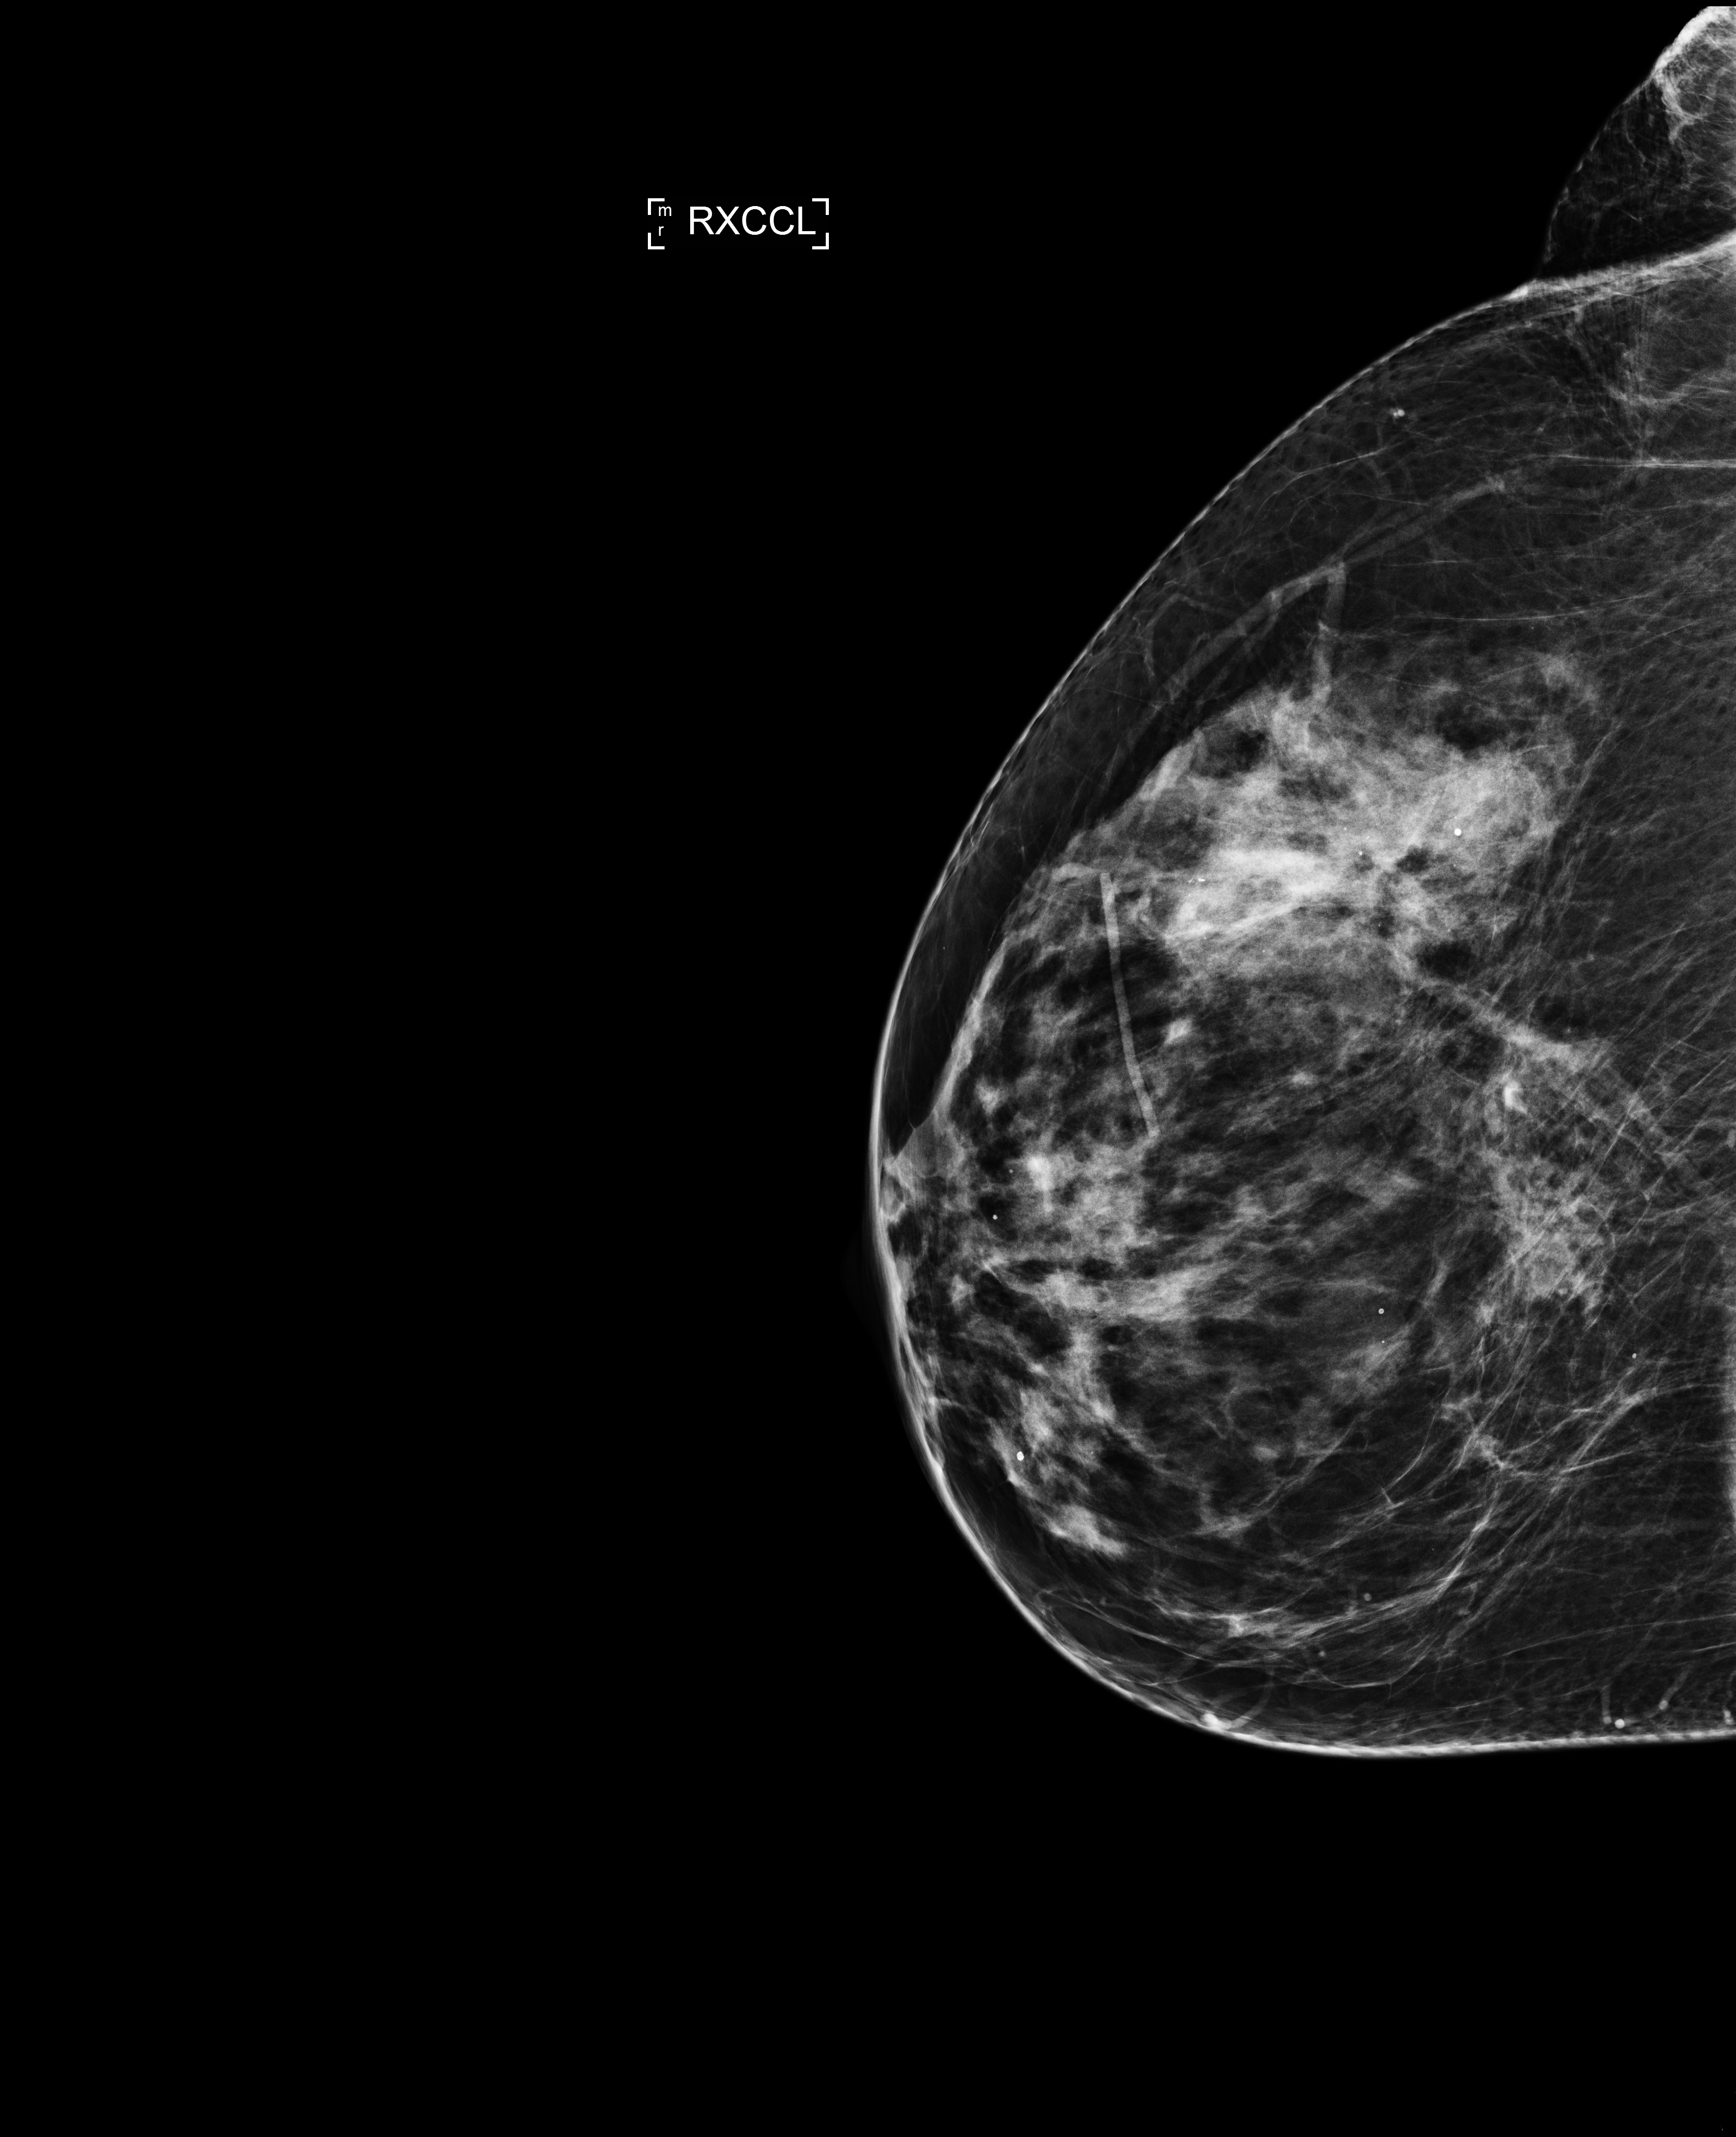
Screening examination, compressed breast thickness 68 mm. Patient: female, 60 years.
Image type: full-field digital mammogram. Breast: right. Projection: laterally exaggerated craniocaudal (XCCL) view.